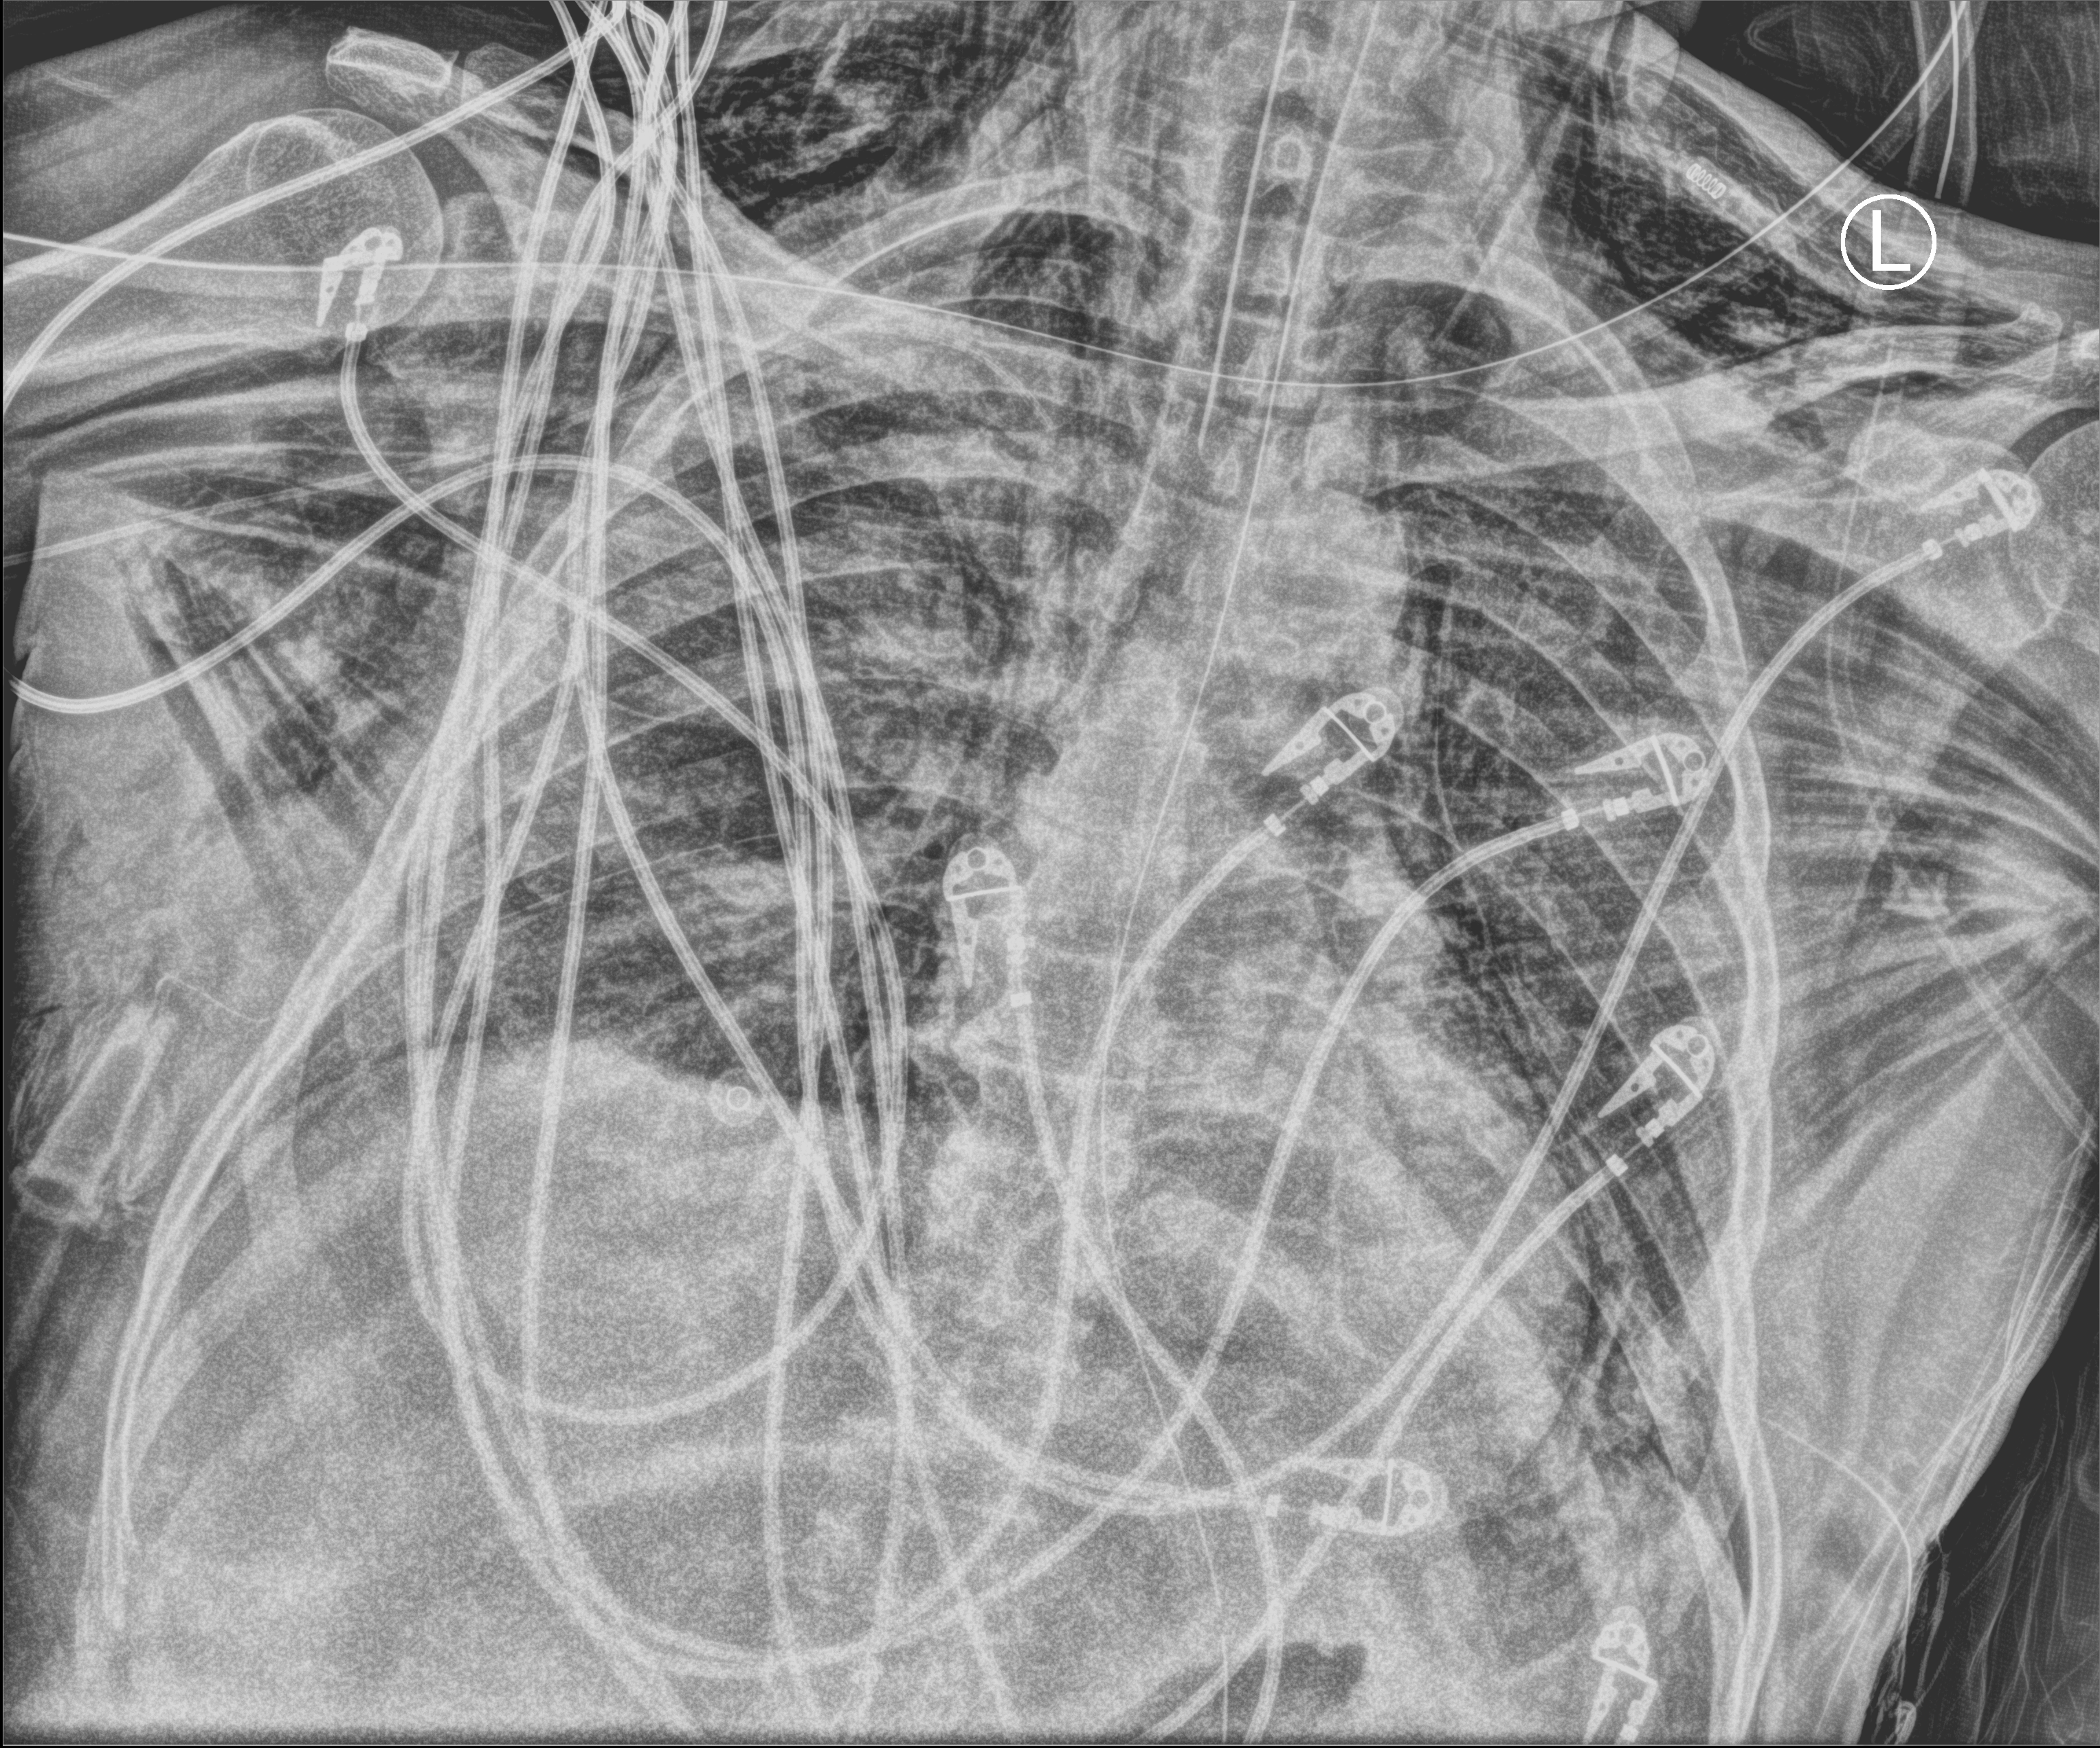
Bedside chest radiograph (computed radiography), anteroposterior (AP) projection. Male patient hospitalised with COVID-19, age 18–59 years.
Admission-level facts for this patient (not findings on this image; timing relative to this image not recorded): admitted to intensive care during this hospital stay: yes; length of hospital stay: 83 days.